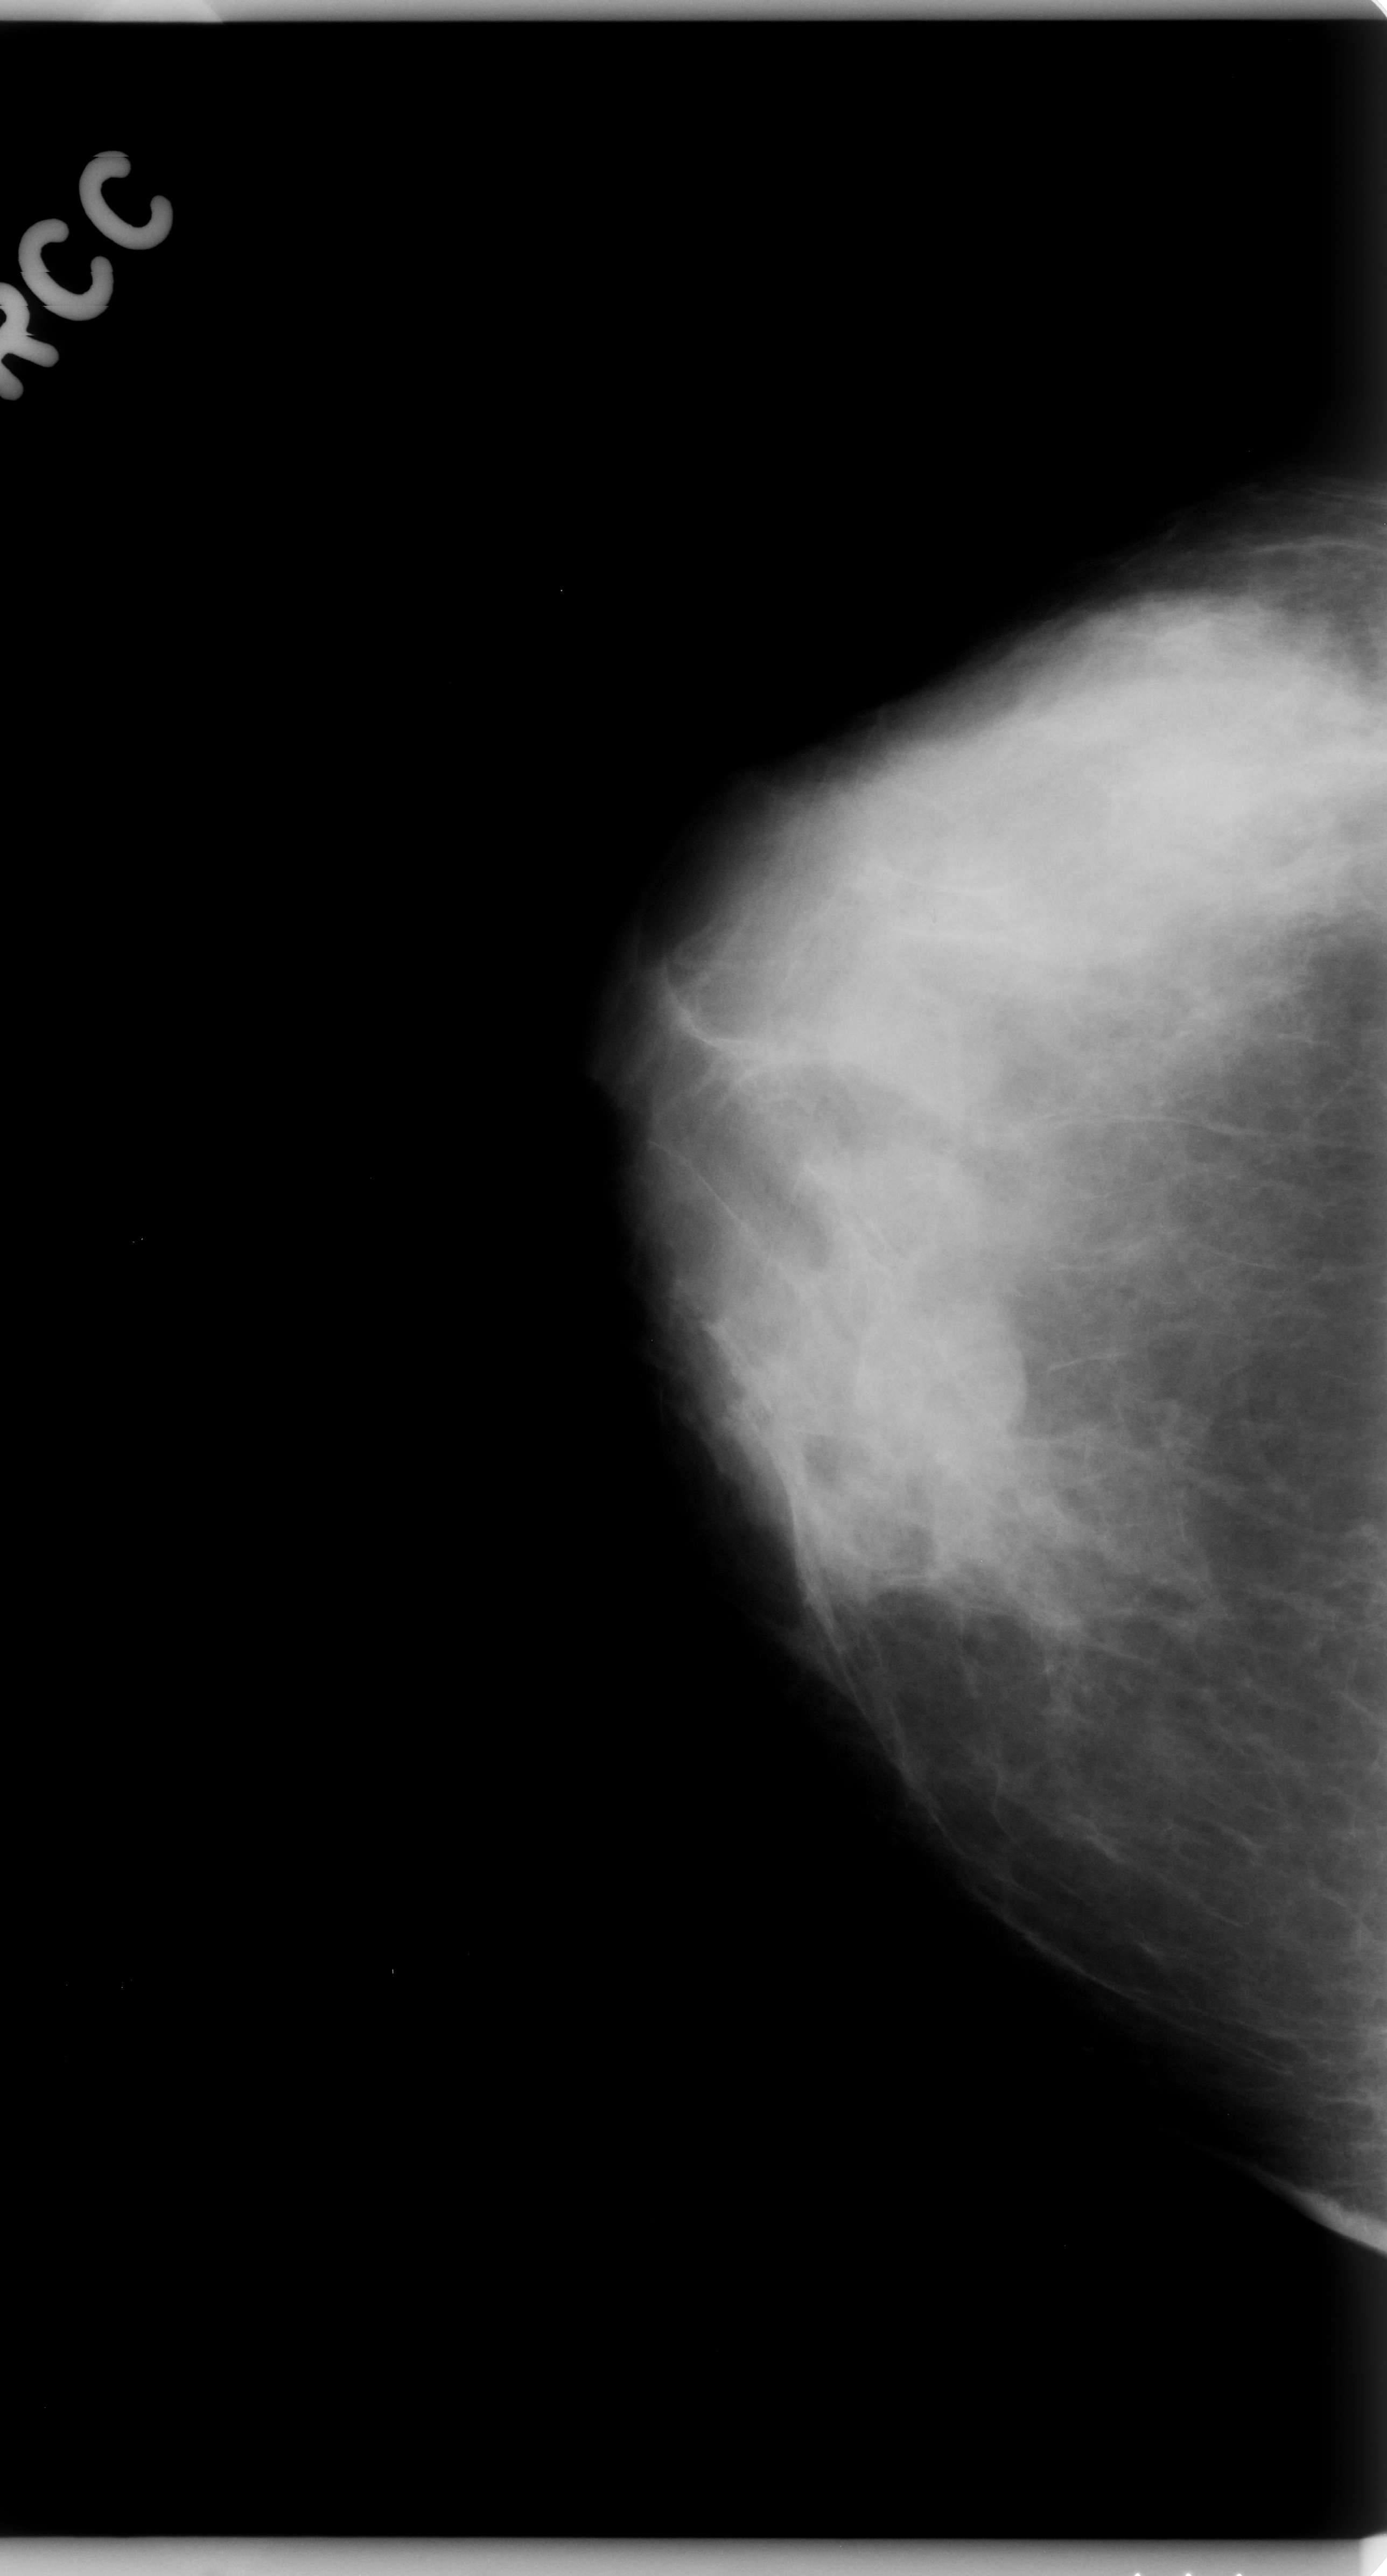
Mammogram (digitized film); right breast; craniocaudal (CC) view; breast composition: heterogeneously dense (BI-RADS density category 3 of 4); 1387 × 2576 image matrix.
Marked abnormalities (boxes around the expert regions of interest):
- mass, shape round, margins obscured; BI-RADS assessment category 3; subtlety rating 4 on a 1 (subtle) to 5 (obvious) scale; pathology (as recorded): benign: bounding box [x1, y1, x2, y2] px = [853, 1304, 1031, 1470]